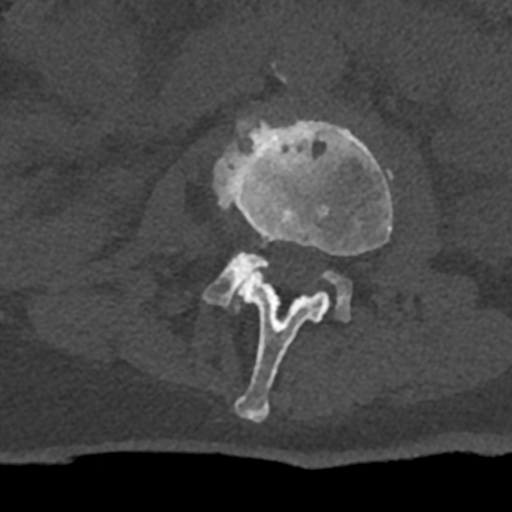
CT including the spine, one axial slice. Position 358 of 797 along the scan axis. Reconstruction kernel Br40s/3. Bone window (W 1800 / L 400 HU). 512 × 512 image matrix. Patient: male, 74 years. Case-level facts recorded for this patient, not image findings: primary cancer: renal.
Outlined on this slice (semi-automatically segmented with operator editing):
- L2 vertebra: bounding box [x1, y1, x2, y2] px = [213, 117, 393, 421]
- L3 vertebra: [203, 252, 352, 321]